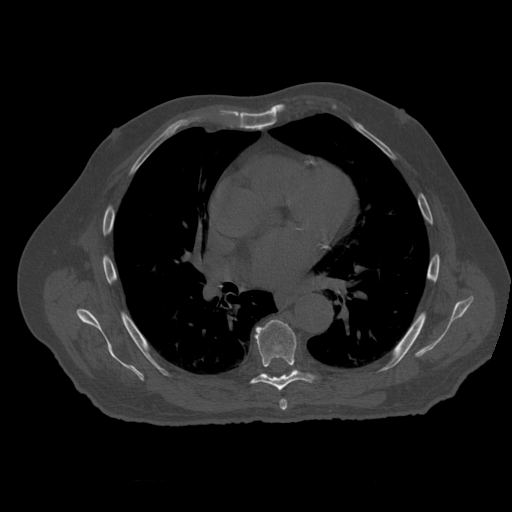
CT including the spine, one axial slice. Position 363 of 399 along the scan axis. Reconstruction kernel STANDARD. 120 kVp. Bone window (W 1800 / L 400 HU). 1.25 mm slice thickness. 512 × 512 image matrix, field of view 407 × 407 mm. Patient age 73 years. From the clinical record (not read from this slice): primary cancer: prostate; vertebrae with lytic lesions (as recorded): L2.
Annotated regions visible in this slice (semi-automatic segmentation, software-assisted and operator-edited):
- T6 vertebra: box from (x=280, y=400) to (x=288, y=411) px
- T7 vertebra: (x=252, y=320)–(x=314, y=391)